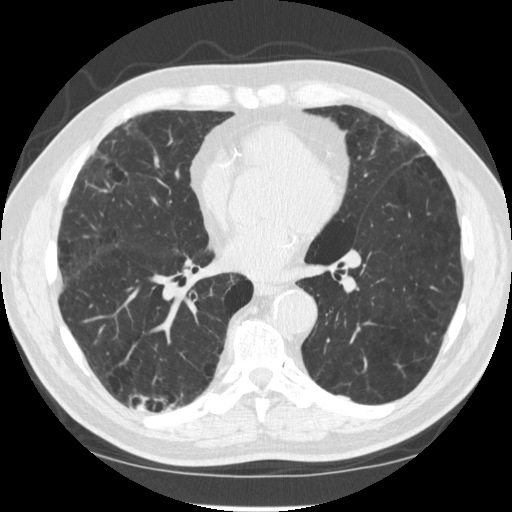
Low-dose screening chest CT, axial slice; second annual screen; lung window (W 1500 / L -600 HU); standard (soft-tissue) reconstruction kernel (STANDARD); slice 156 of 303 in the series; 512 × 512 image matrix. Male, age 70 years at enrolment. Former smoker at enrolment.
Expert reader's lesion annotation, bounding box (x1, y1, x2, y2) in pixels: (123, 375, 174, 432). The screening reader recorded 2 non-calcified nodules or masses ≥4 mm on this exam (right lower lobe, right lower lobe); which of them this box marks is not recorded. Official screen result: negative screen, significant abnormalities not suspicious for lung cancer. Participant outcome: lung cancer diagnosed 617 days after this screen — squamous cell carcinoma, NOS, right upper lobe, poorly differentiated (G3), stage IV (AJCC 6th edition).